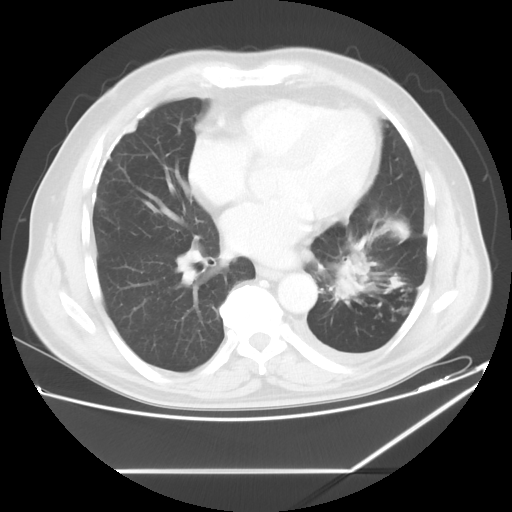
Chest CT, one axial slice; position 26 of 60 along the scan axis; reconstruction kernel STANDARD; lung window (W 1500 / L -600 HU); 5 mm slice thickness; 512 × 512 image matrix. Male patient, age 62 years. Case-level facts recorded for this patient, not image findings: clinical TNM (as recorded): T3 N0 M1.
Outlined on this slice (rectangle marked by the reading radiologist):
- lung tumour (recorded histology: adenocarcinoma): bounding box (x1, y1, x2, y2) in pixels: (340, 251, 369, 304)